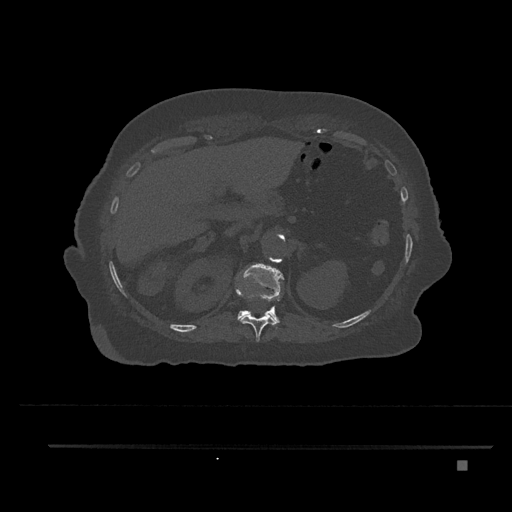
CT including the spine, one axial slice; position 292 of 797 along the scan axis; reconstruction kernel Br40s/3; bone window (W 1800 / L 400 HU); 0.5 mm slice thickness; 512 × 512 image matrix, field of view 437 × 437 mm. Patient: female, 76 years. From the clinical record (not read from this slice): primary cancer: lung; vertebrae with lytic lesions (as recorded): T11, L3.
Outlined on this slice (semi-automatically segmented with operator editing):
- T11 vertebra: bounding box (x1, y1, x2, y2) in pixels: (236, 288, 277, 342)
- T12 vertebra: (237, 264, 284, 324)